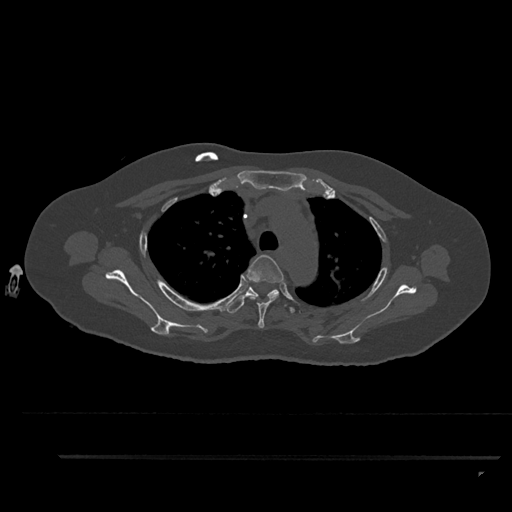
CT including the spine, one axial slice; slice 665 of 797 in the series (ordered by position); reconstruction kernel Br40s/3; bone window (W 1800 / L 400 HU); 0.5 mm slice thickness; 512 × 512 image matrix, field of view 408 × 408 mm. Female patient, age 44 years. From the clinical record (not read from this slice): primary cancer: renal.
Structures marked on this image (semi-automatically segmented with operator editing):
- T3 vertebra: bounding box [x1, y1, x2, y2] px = [243, 255, 284, 328]
- T4 vertebra: [227, 286, 295, 313]